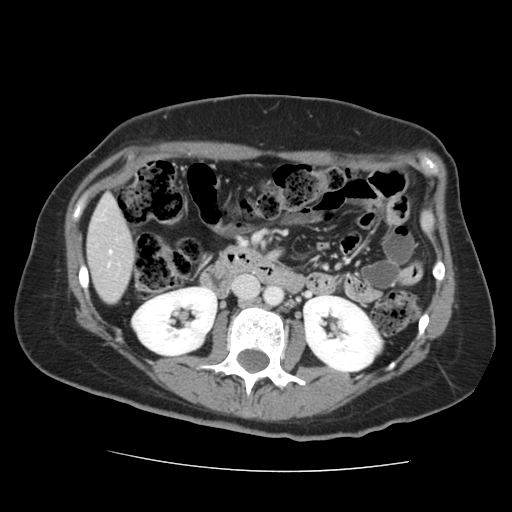
Contrast-enhanced abdominal CT, one axial slice. Slice 53 of 144 in the series (ordered by position). 120 kVp. Intravenous contrast given. Soft-tissue window (W 400 / L 40 HU). 2.5 mm slice thickness. 512 × 512 image matrix, field of view 333 × 333 mm. Female patient, age 46 years. From the clinical record (not read from this slice): diagnosis: colorectal cancer liver metastases, imaged before liver resection; multiple liver metastases: no.
Outlined on this slice (outlined manually by an expert reader):
- liver: bounding box (x1, y1, x2, y2) in pixels: (89, 198, 133, 302)
- planned liver remnant (the part of the liver to remain after resection): (89, 198, 133, 269)
- portal vein (with intrahepatic branches): (109, 251, 111, 254)